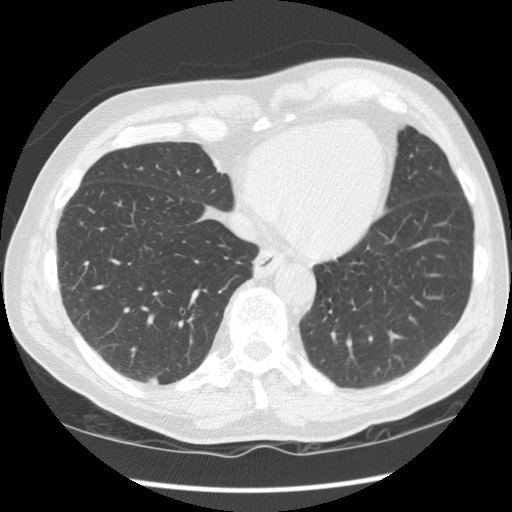
Low-dose screening chest CT, axial slice. First (baseline) screen. Lung window (W 1500 / L -600 HU). 2.5 mm slice thickness. 120 kVp. Slice 28 of 83 in the series. Male, age 71 years at enrolment. Current smoker at enrolment.
• Expert reader's lesion annotation, bounding box (x1, y1, x2, y2) in pixels: (134, 366, 170, 397).
• Reader record for this screening exam (exam-level; its link to the box is not recorded): non-calcified nodule or mass ≥4 mm, right upper lobe, 26 × 15 mm, smooth margins, mixed attenuation.
• Official screen result: positive, change unspecified: nodule(s) >= 4 mm or enlarging nodule(s), mass(es), or other non-specific abnormalities suspicious for lung cancer.
• Participant outcome: lung cancer diagnosed 357 days after this screen — squamous cell carcinoma, NOS, right lower lobe, moderately differentiated (G2), stage IA (AJCC 6th edition), 27 mm at pathology.